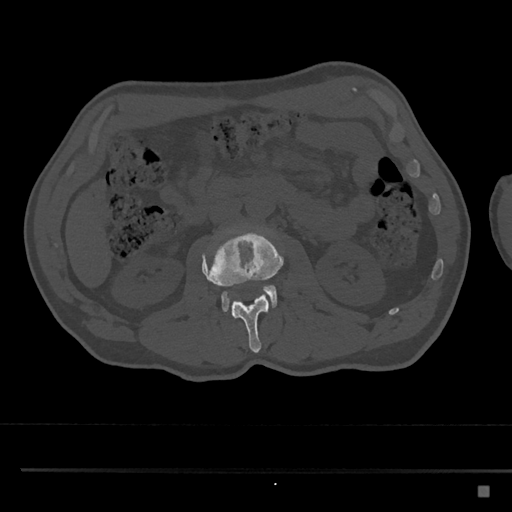
CT including the spine, one axial slice. Position 739 of 797 along the scan axis. 120 kVp. Bone window (W 1800 / L 400 HU). 512 × 512 image matrix, field of view 391 × 391 mm. Male patient, age 59 years. From the clinical record (not read from this slice): primary cancer: prostate.
Annotated regions visible in this slice (semi-automatic segmentation, software-assisted and operator-edited):
- L2 vertebra: bounding box <201,229,284,353> (left, top, right, bottom; pixels)
- L3 vertebra: <221,284,278,313>